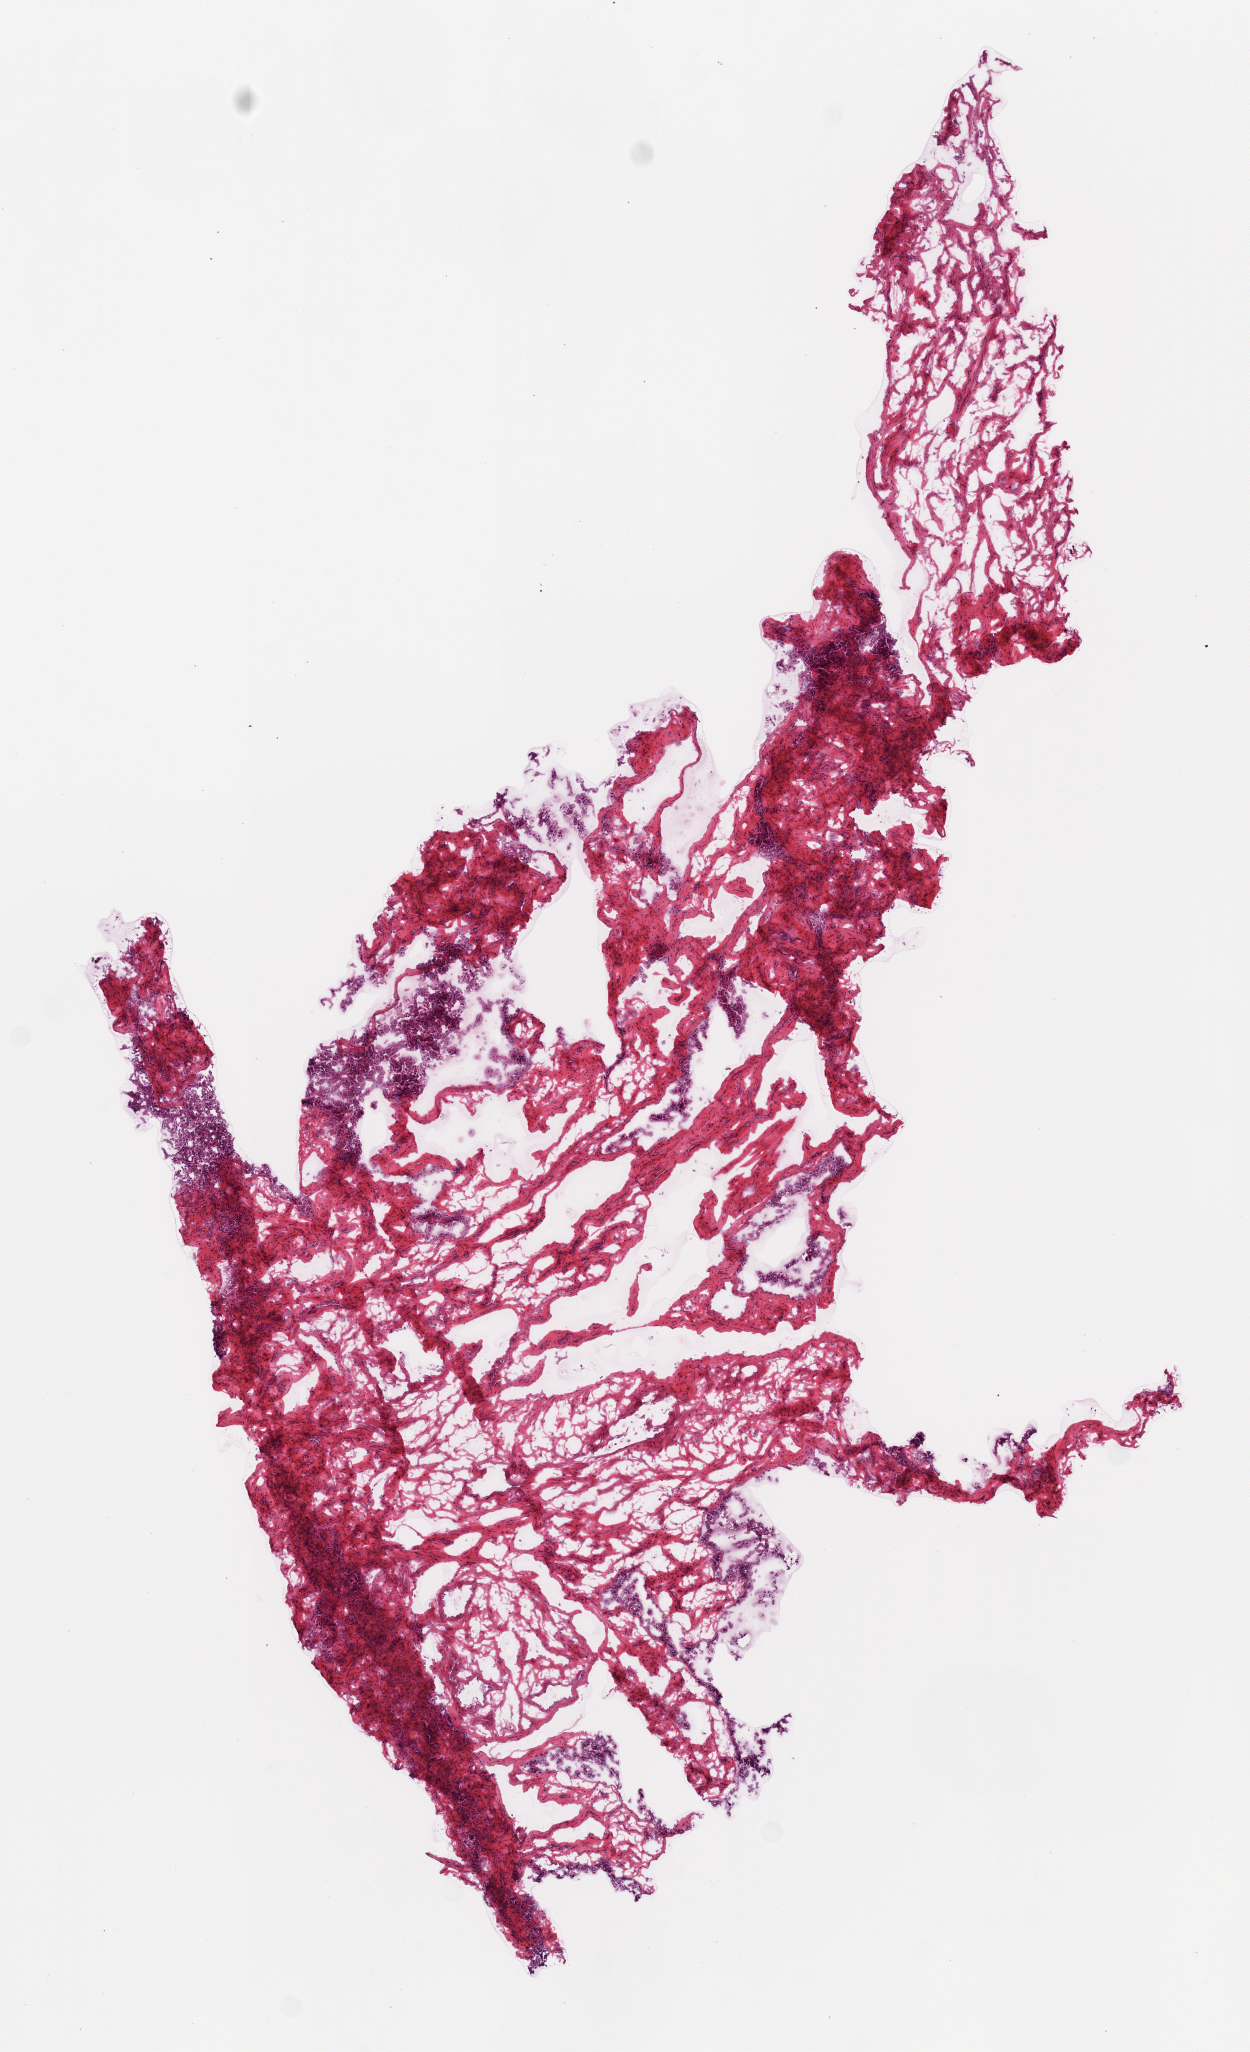
Digitized H&E tissue section (whole slide), shown as a low-resolution overview of the whole scanned area (about 5.0 x 8.2 mm, slide scanned at 20x), frozen section, solid tissue normal (non-tumour tissue) sample from the ovary. Female, age 48 years at initial diagnosis.
This section: solid tissue normal (non-tumour) sample from the same patient. Patient diagnosis: Serous cystadenocarcinoma, NOS.